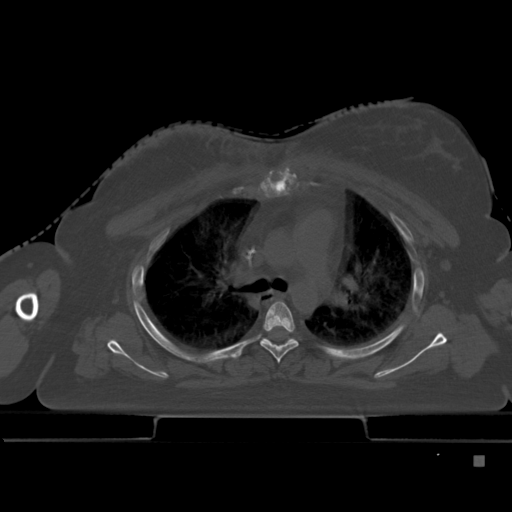
CT including the spine, one axial slice; slice 330 of 495 in the series (ordered by position); bone window (W 1800 / L 400 HU); 1.5 mm slice thickness; 512 × 512 image matrix, field of view 404 × 404 mm. Patient: female, 33 years. Case-level facts recorded for this patient, not image findings: primary cancer: breast; vertebrae with lytic lesions (as recorded): T1.
Annotated regions visible in this slice (semi-automatic segmentation, software-assisted and operator-edited):
- T4 vertebra: bounding box [x1, y1, x2, y2] px = [260, 301, 298, 364]
- T5 vertebra: [261, 337, 296, 346]